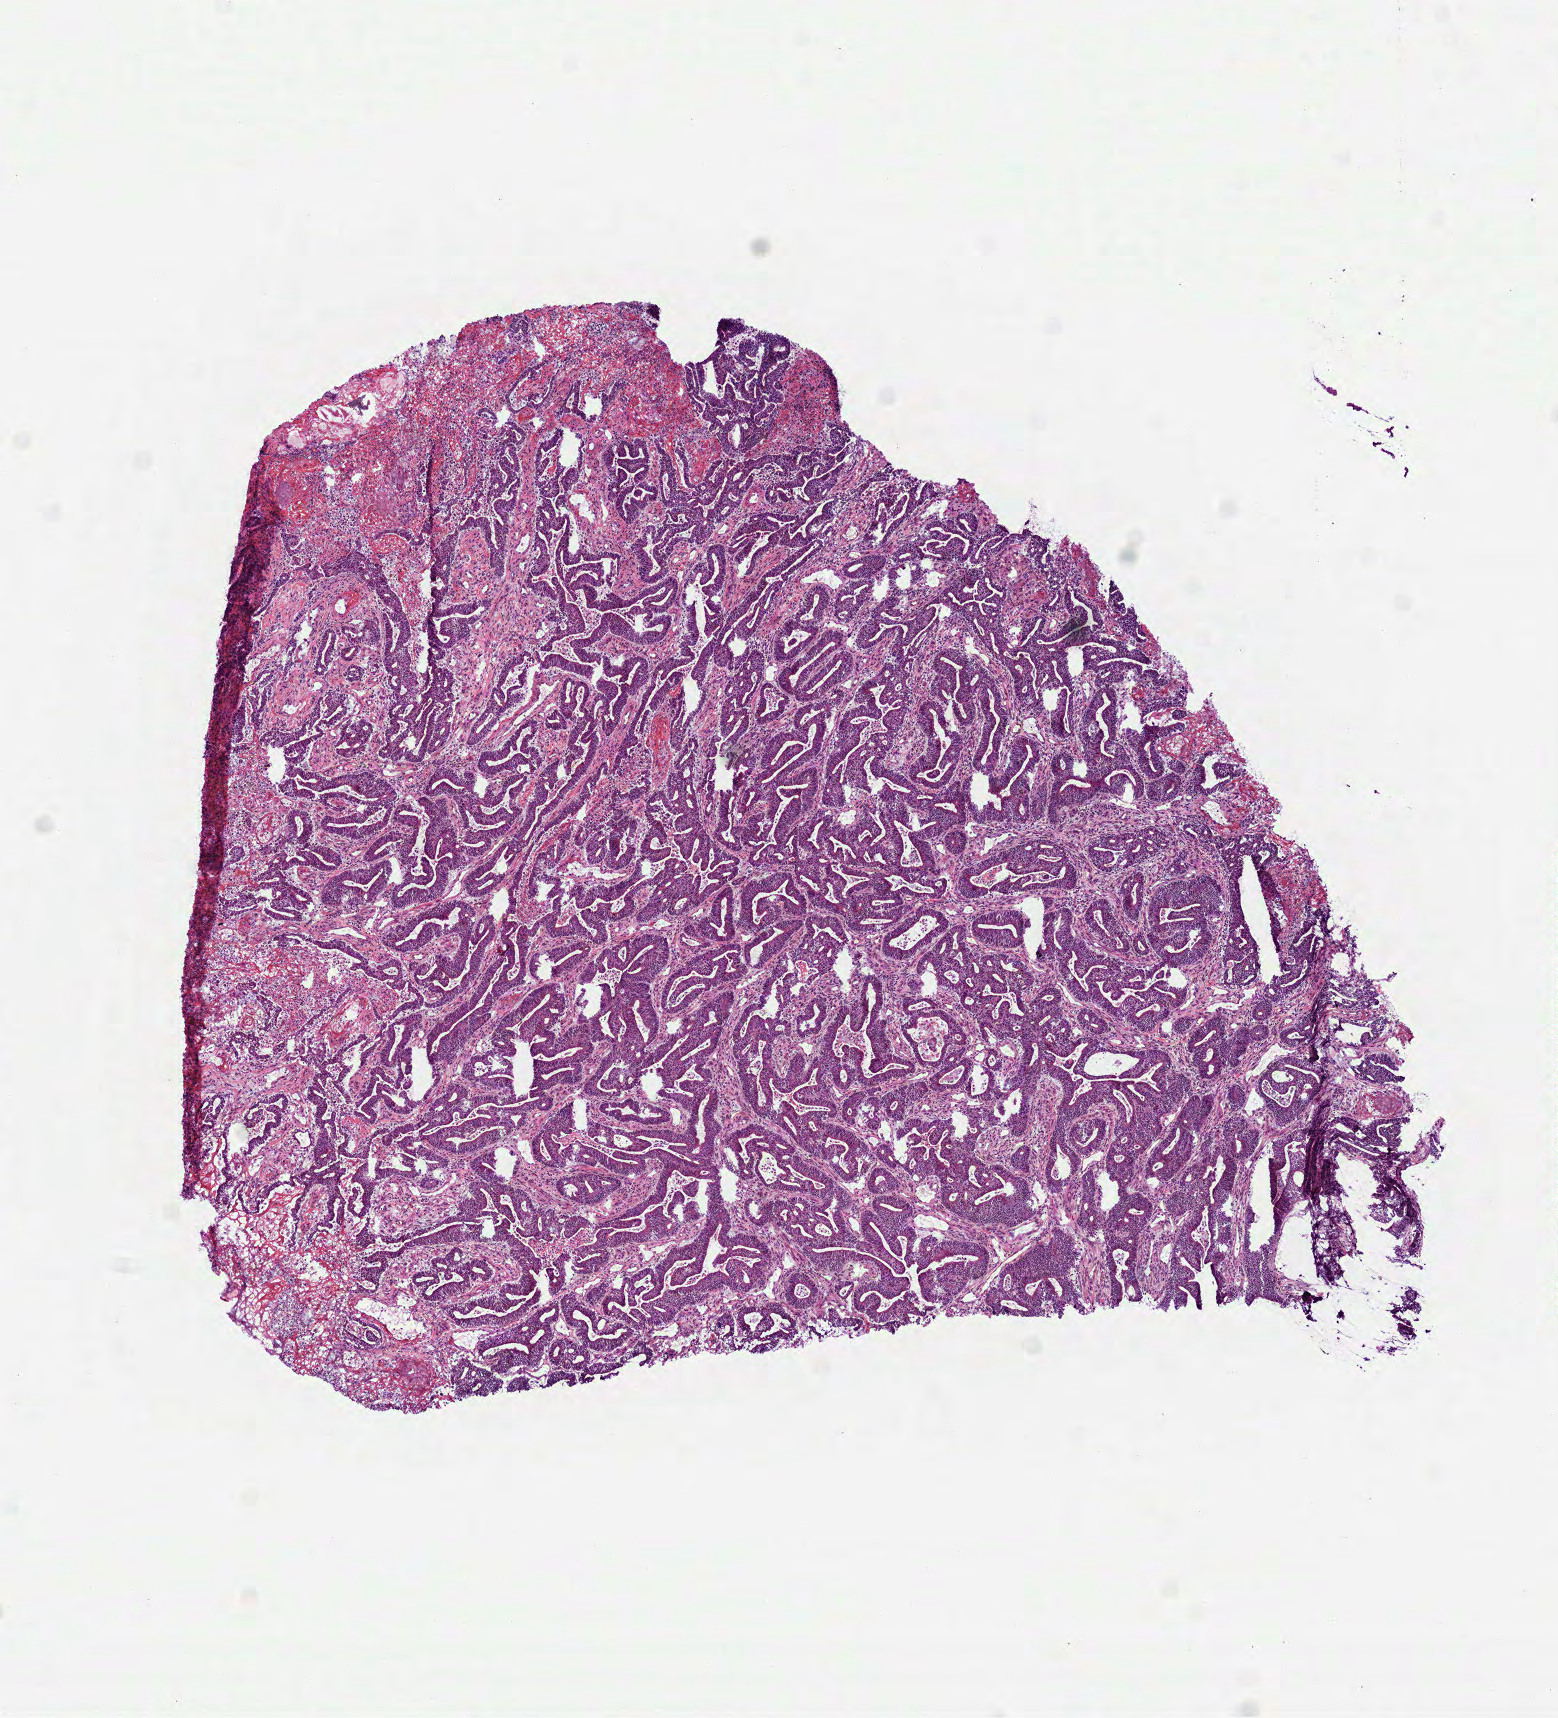
Digitized Hematoxylin and eosin (H&E) stained tissue section (whole slide) — whole scanned area (about 6.3 x 6.9 mm, acquisition: 40x scan) shown as a low-resolution overview, frozen section, sample: primary tumour, stomach. Patient sex: male. Histologic grade: G2 (moderately differentiated). Composition of this section per pathologist review: tumour cells 88%, tumour nuclei 80%, normal cells 0%, stromal cells 12%, necrosis 0%.
- lymph nodes positive (case pathology): 2 of 7 examined
- AJCC pathologic stage: I
- histologic diagnosis: Adenocarcinoma, NOS (gastric antrum)